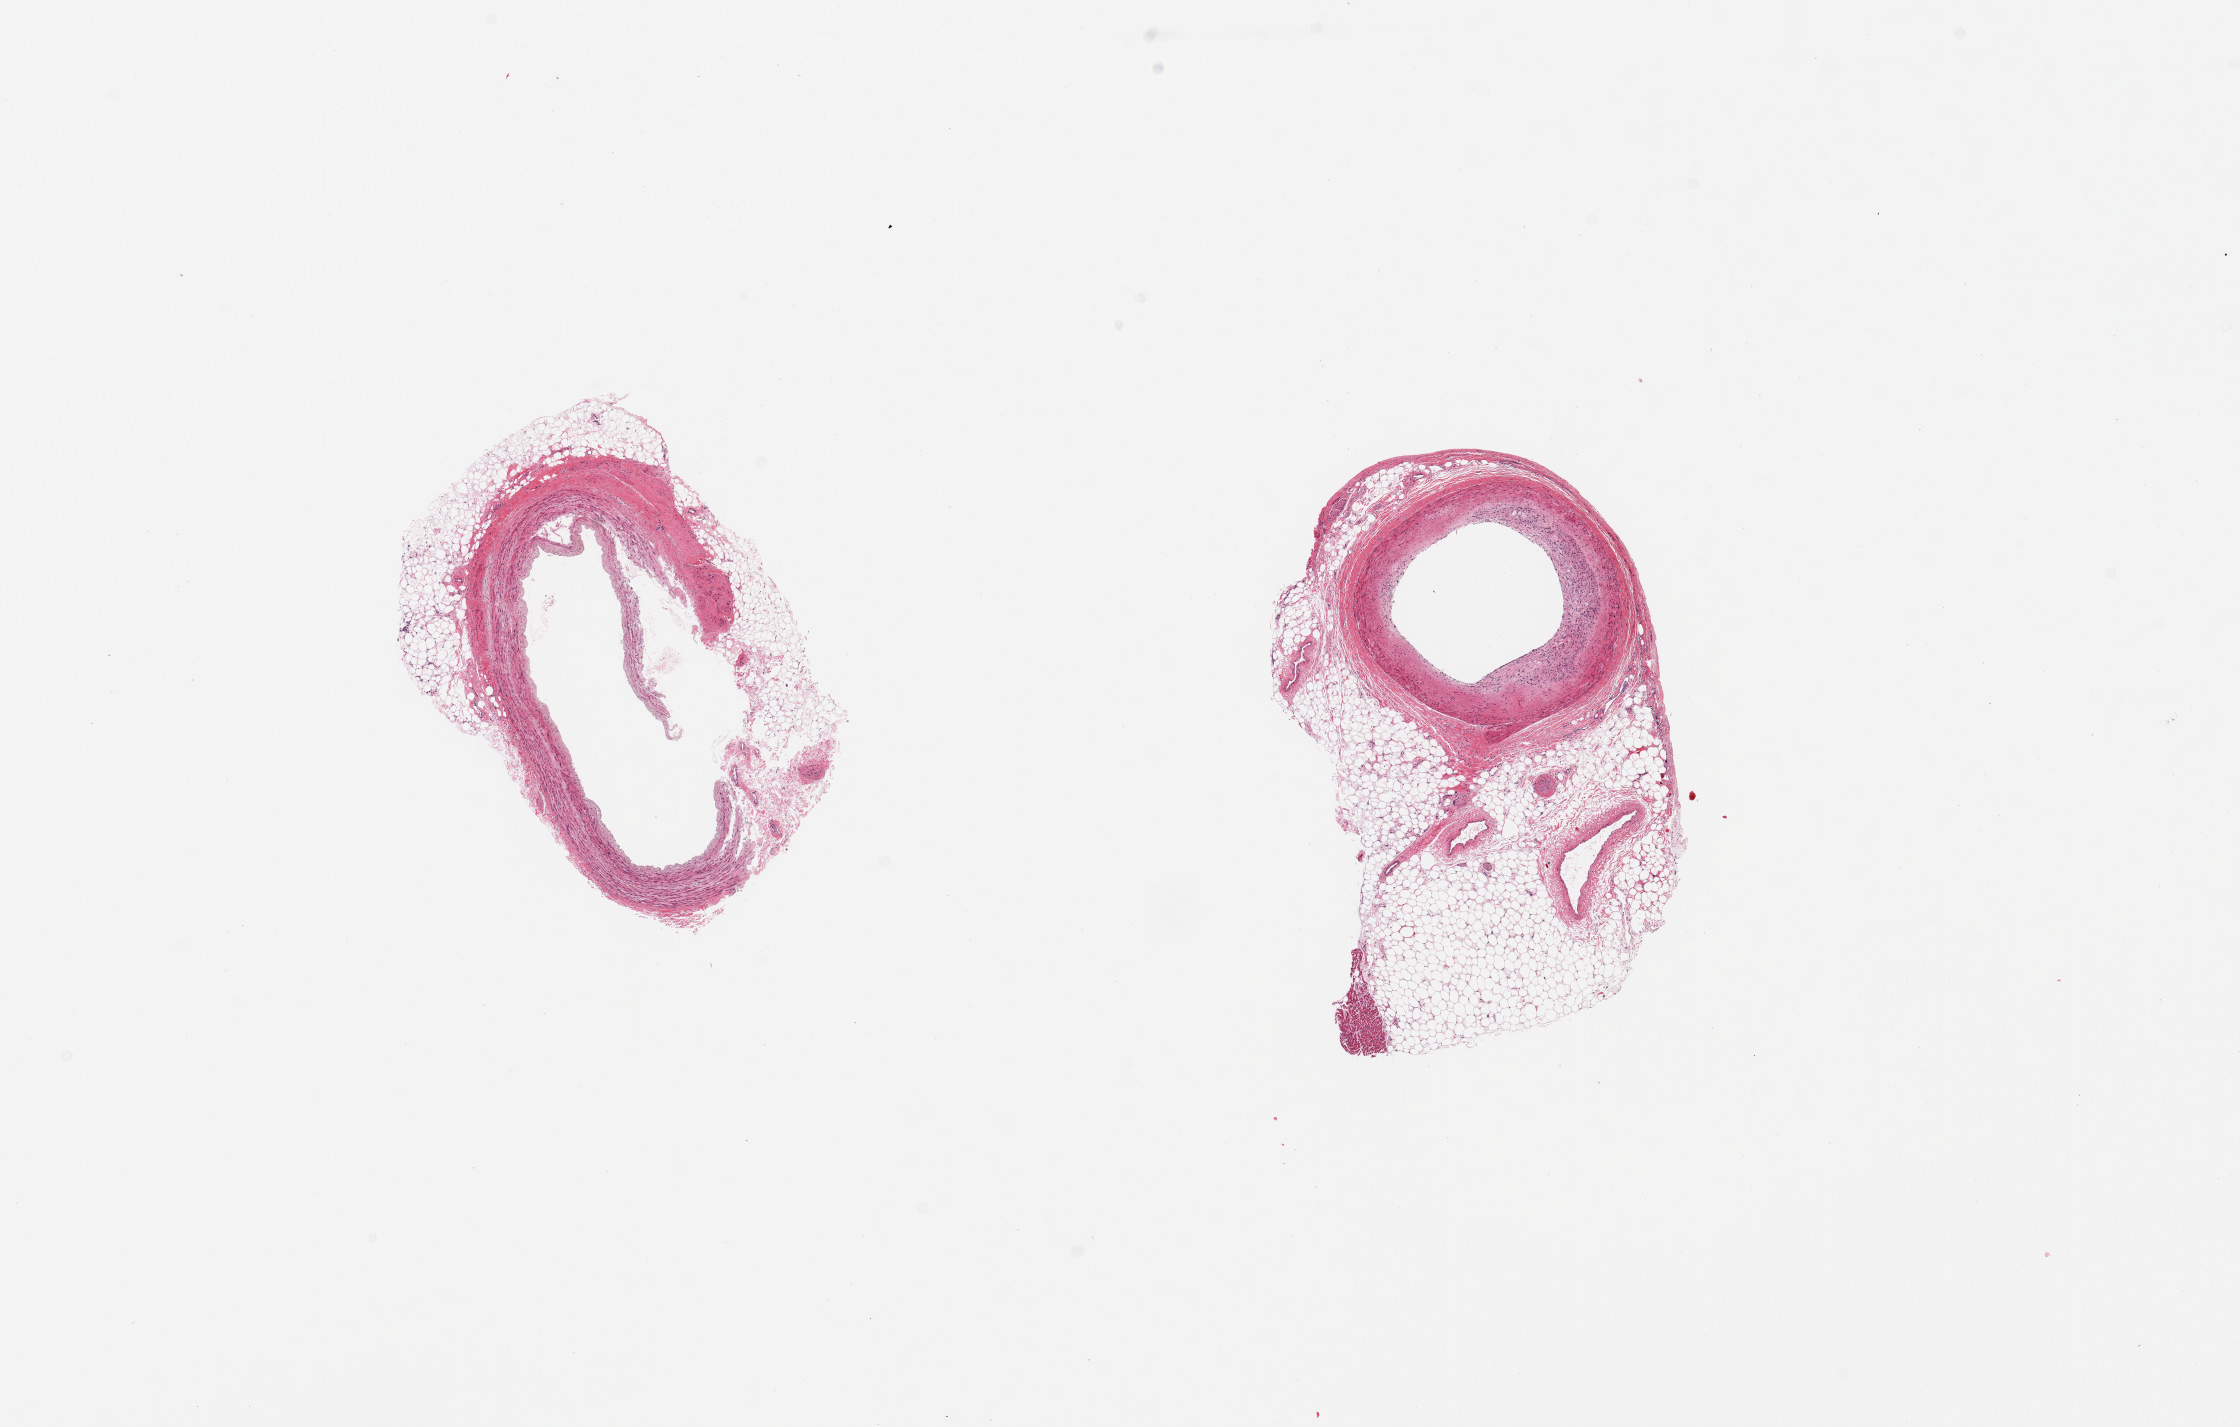
H&E whole-slide image — low-resolution overview of the scanned area, about 17.7 x 11.3 mm; PAXgene-fixed paraffin-embedded (PFPE) section; target tissue: coronary artery; tissue donor sample.
Pathologist's review note for this sample: 2 pieces; both include abundant attached fat/vessels, myocardium (50 and 75%), atherosclerosis.